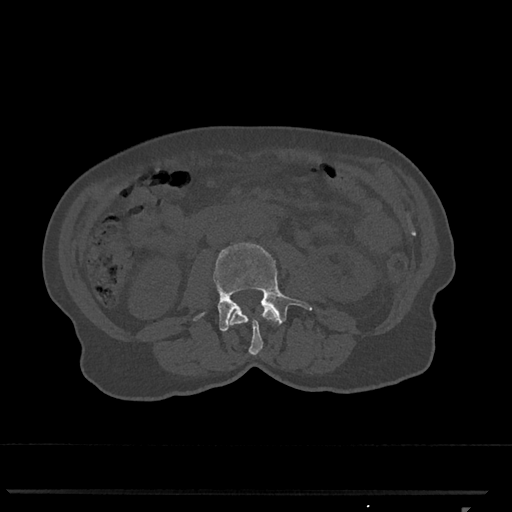
CT including the spine, one axial slice. Position 294 of 793 along the scan axis. Bone window (W 1800 / L 400 HU). 0.5 mm slice thickness. 512 × 512 image matrix, field of view 380 × 380 mm. Female patient, age 62 years. Case-level facts recorded for this patient, not image findings: primary cancer: renal.
Outlined on this slice (semi-automatically segmented with operator editing):
- L2 vertebra: bounding box (x1, y1, x2, y2) in pixels: (228, 306, 278, 355)
- L3 vertebra: (194, 242, 312, 331)